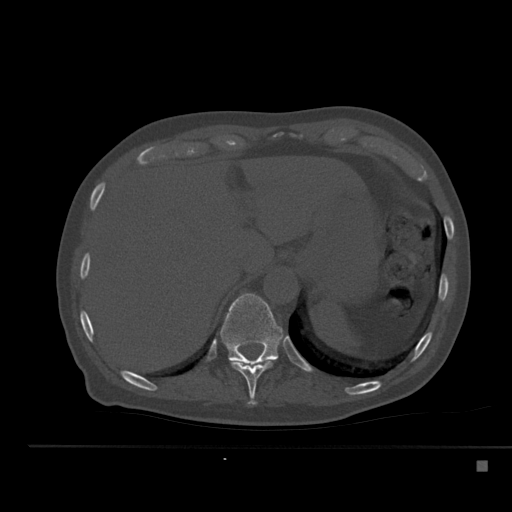
CT including the spine, one axial slice. 120 kVp. Bone window (W 1800 / L 400 HU). 1.5 mm slice thickness. 512 × 512 image matrix. Patient: male, 70 years. From the clinical record (not read from this slice): primary cancer: renal.
Outlined on this slice (semi-automatically segmented with operator editing):
- T10 vertebra: bounding box (x1, y1, x2, y2) in pixels: (229, 360, 275, 405)
- T11 vertebra: (220, 293, 283, 364)